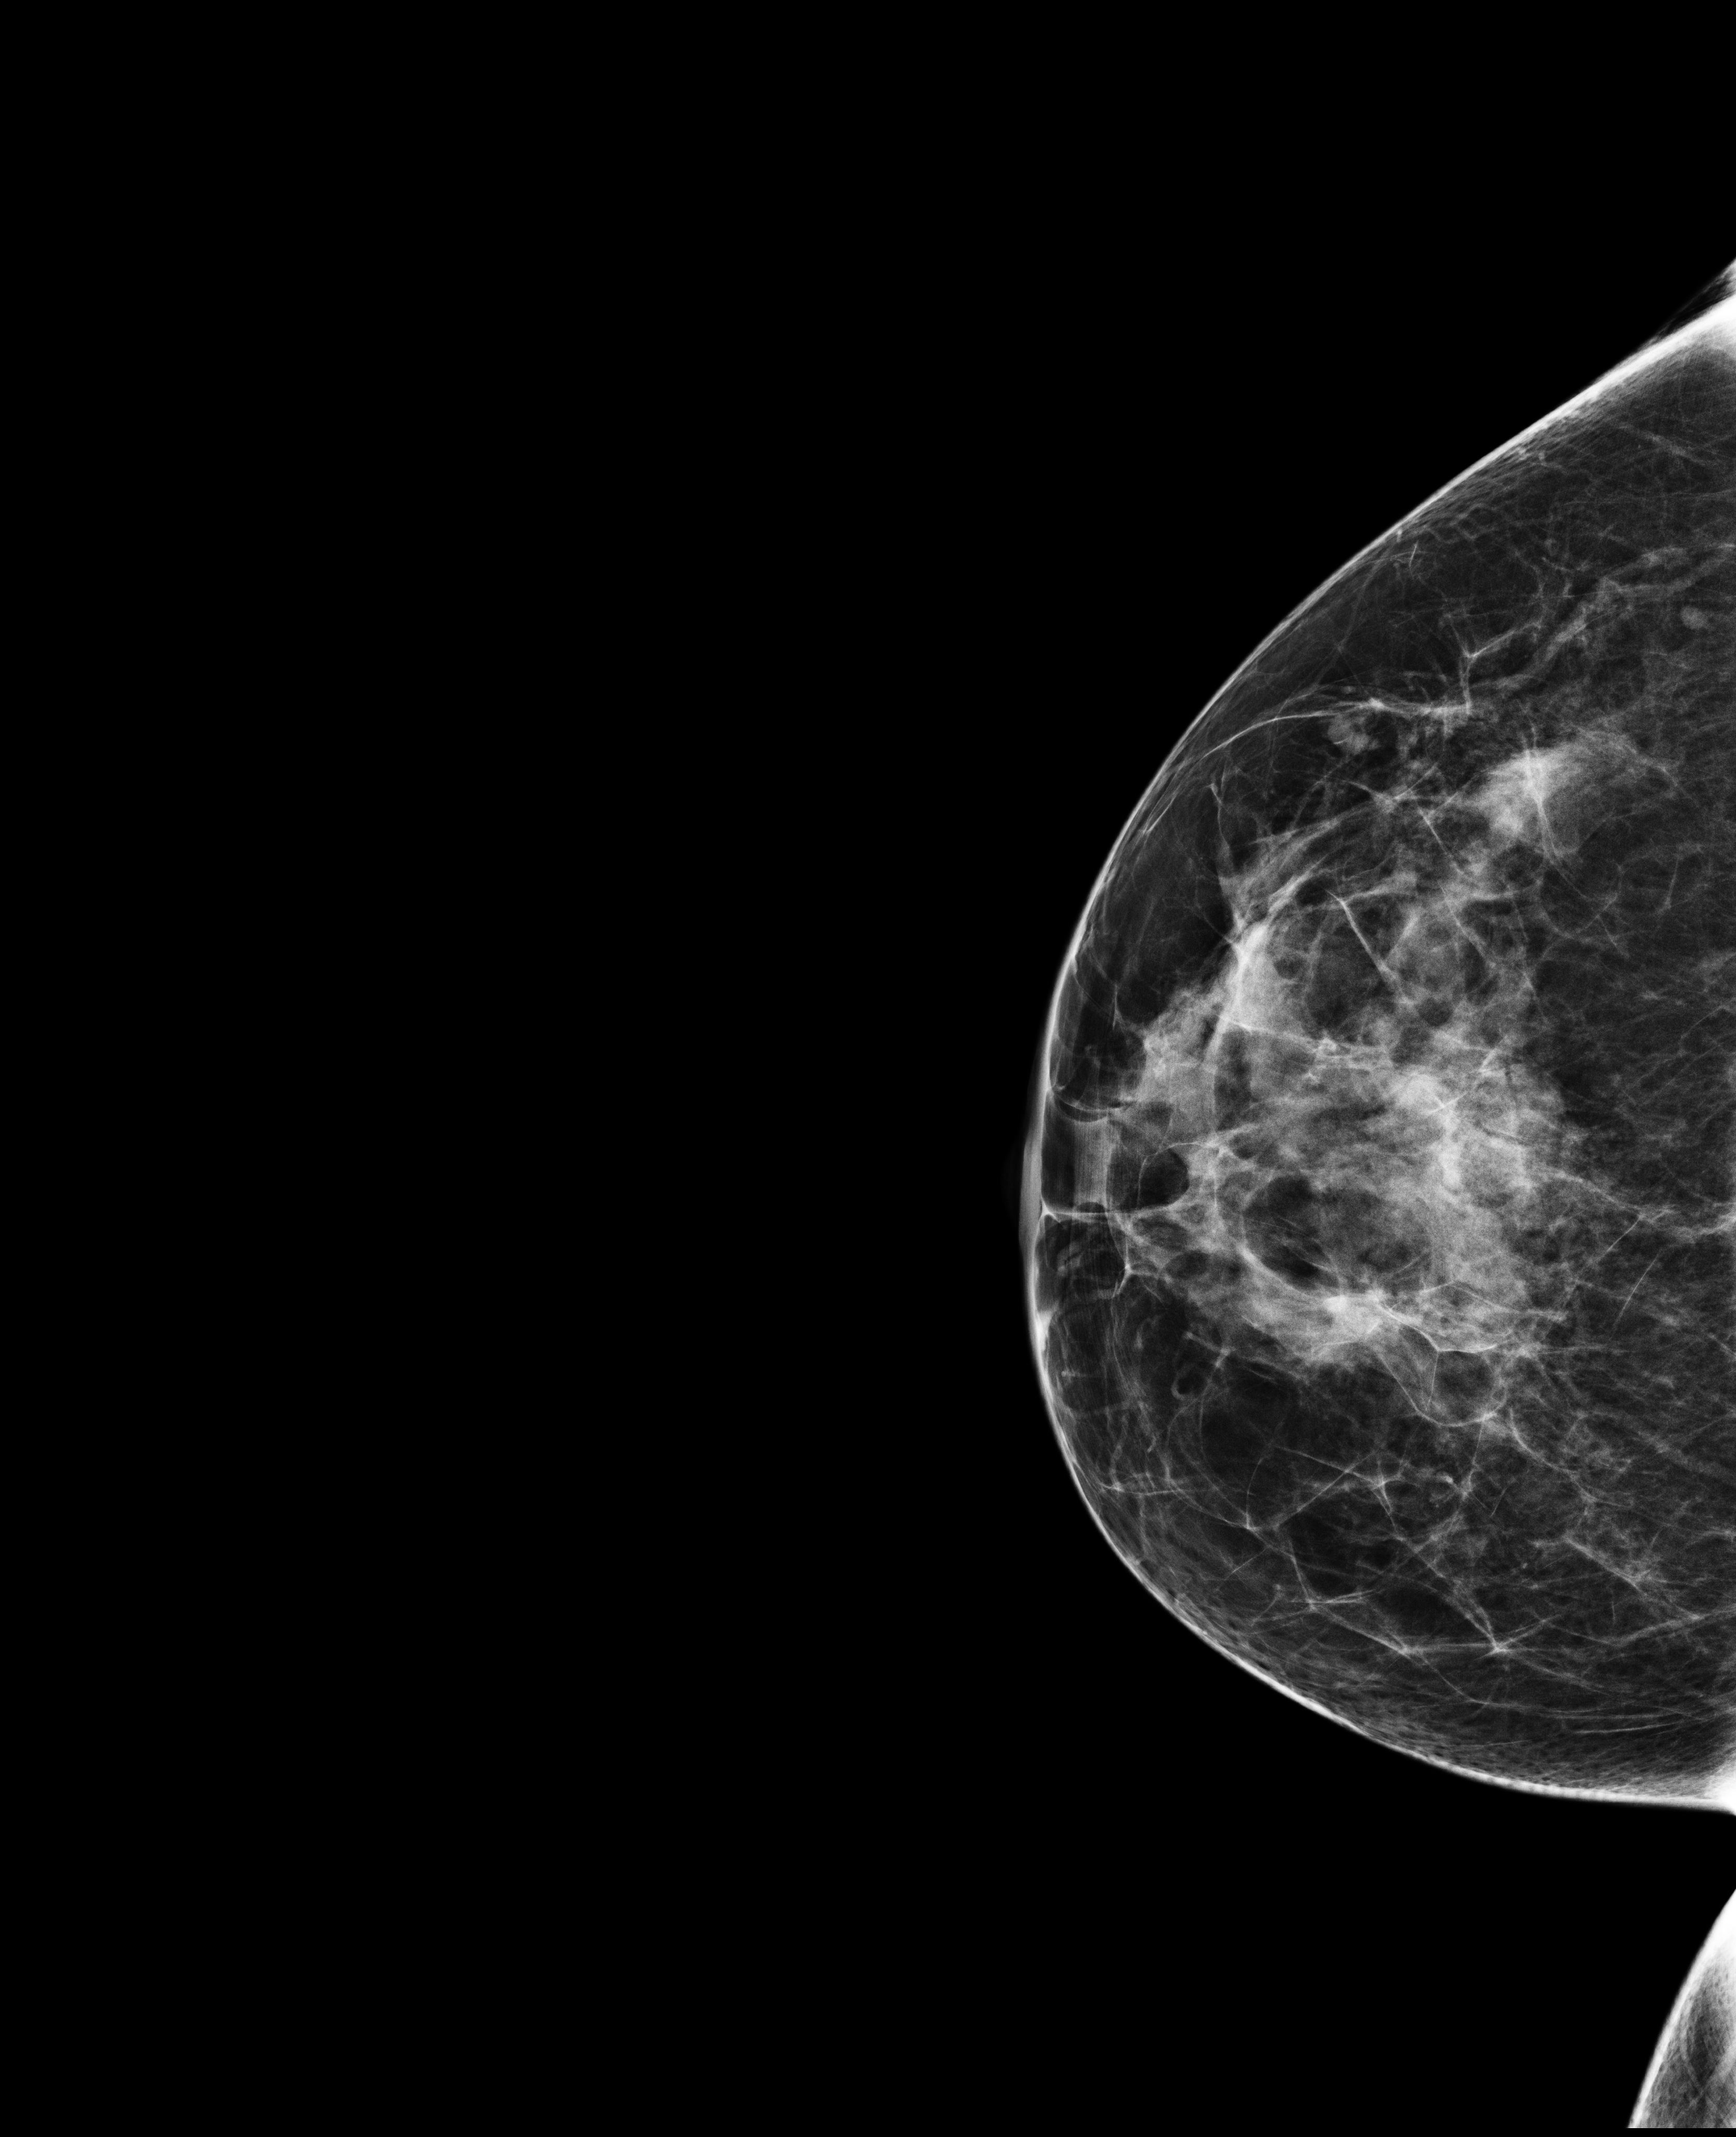
Annual screening mammography examination, compressed breast thickness 58 mm. Female patient, age 43 years.
Image type: full-field digital mammogram. Breast: right. Projection: cranio-caudal projection.